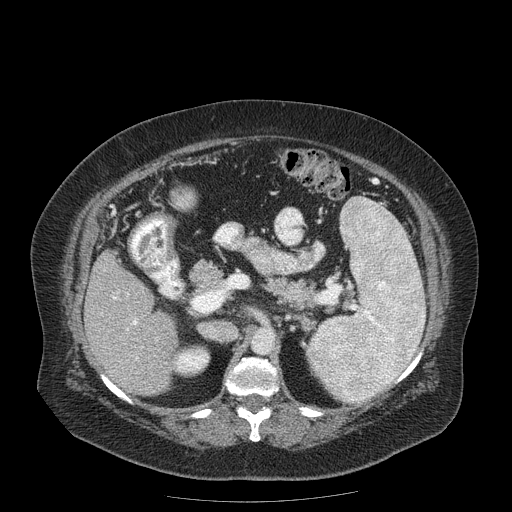
Contrast-enhanced abdominal CT (liver protocol), one axial slice. Slice 87 of 204 in the series (ordered by position). Reconstruction kernel STANDARD. 120 kVp. Soft-tissue window (W 400 / L 40 HU). 512 × 512 image matrix, field of view 440 × 440 mm. Case-level facts recorded for this patient, not image findings: diagnosis: hepatocellular carcinoma (patient treated with transarterial chemoembolisation; whether this scan precedes or follows treatment is not stated here); TNM stage (as recorded): Stage-IIIB; Child-Pugh class: A; tumour differentiation: well differentiated.
Structures marked on this image (semi-automatic segmentation, software-assisted and operator-edited):
- liver parenchyma outside the tumour (the mass and vessels are separate outlines, so this box may not span the whole liver): bounding box <84,251,178,396> (left, top, right, bottom; pixels)
- liver vessels: <113,297,138,360>